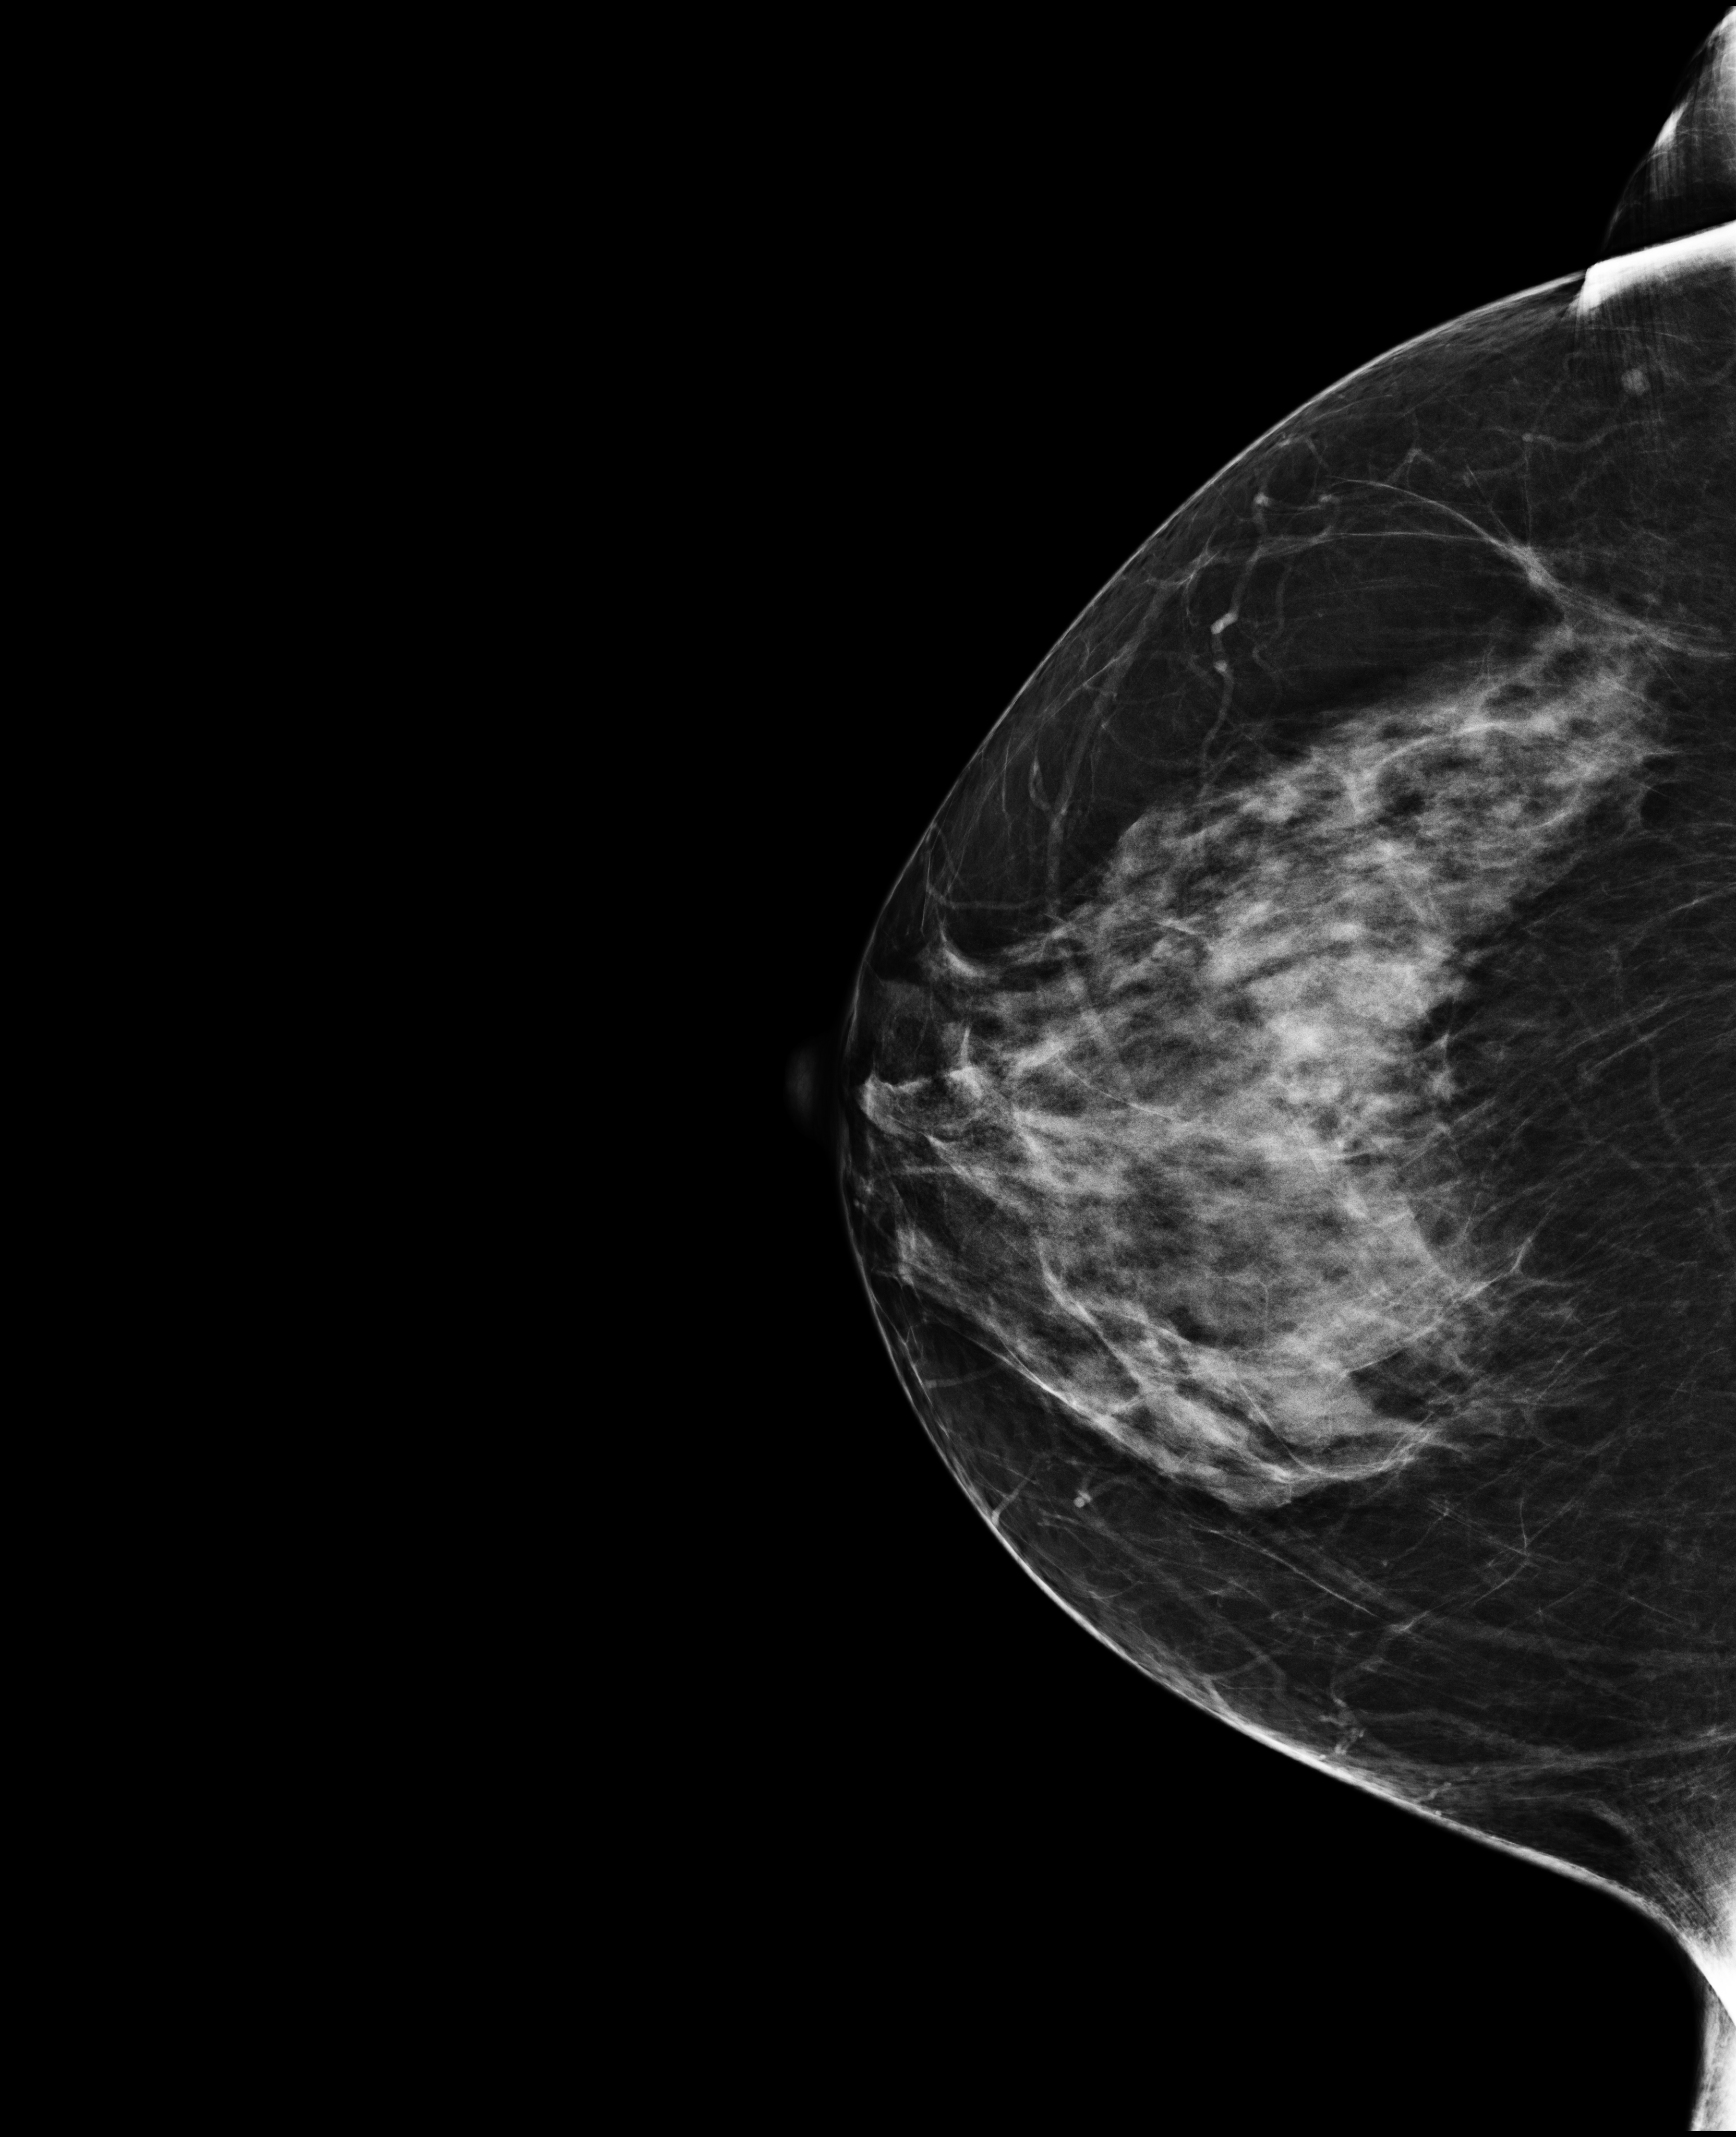
Full-field digital mammogram (FFDM), right breast, CC view, screening examination. Patient: female, 59 years.
BI-RADS breast density category at the screening exam (both breasts, scale 1–4): 3. Final BI-RADS category for the screening round (tomosynthesis exam, both breasts): category 2. Recall: no recall after this screen.